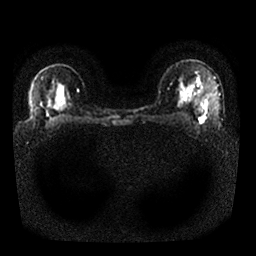
Breast MRI, one axial slice; slice 18 of 25 in the series (ordered by position); diffusion-weighted series; image 2 of 4 stored at this slice position (different b-values; order by instance number); 1.5 T; 4 mm slice thickness; 256 × 256 image matrix, field of view 330 × 330 mm. Female patient.
Structures marked on this image (manually delineated by an expert):
- tumour on diffusion-weighted imaging: bounding box (x1, y1, x2, y2) in pixels: (200, 119, 202, 122)